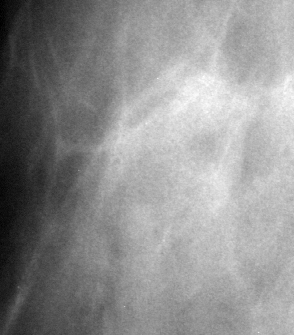
Crop from a digitized film mammogram around one marked abnormality, right breast, MLO view.
Mass, shape irregular, margins ill defined; BI-RADS assessment category 4; subtlety rating 2 on a 1 (subtle) to 5 (obvious) scale; pathology (as recorded): benign.